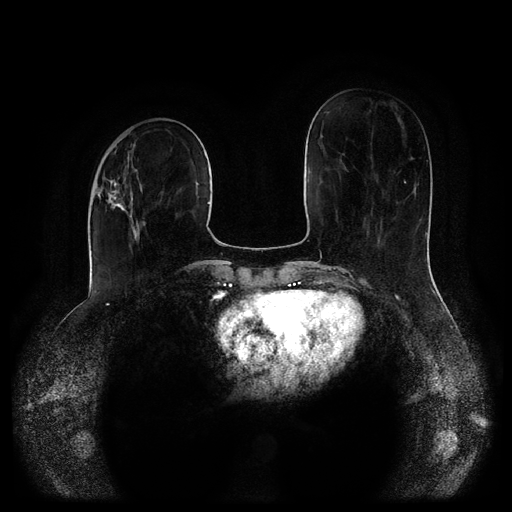
Breast MRI (dynamic contrast-enhanced, multi-phase), one axial slice; slice 35 of 116 in the series (ordered by position); dynamic contrast-enhanced series, time point 2 of 5 at this slice position (early post-contrast); 1.5 T; TE 2.6 ms, TR 5.2 ms; 2 mm slice thickness; 512 × 512 image matrix, field of view 380 × 380 mm. Female patient, age 52 years.
Outlined on this slice (semi-automatic segmentation, software-assisted and operator-edited):
- breast lesion (labelled 'tumour' in the annotation; benign lesions carry a separate 'benign' label): bounding box [x1, y1, x2, y2] px = [103, 172, 146, 250]